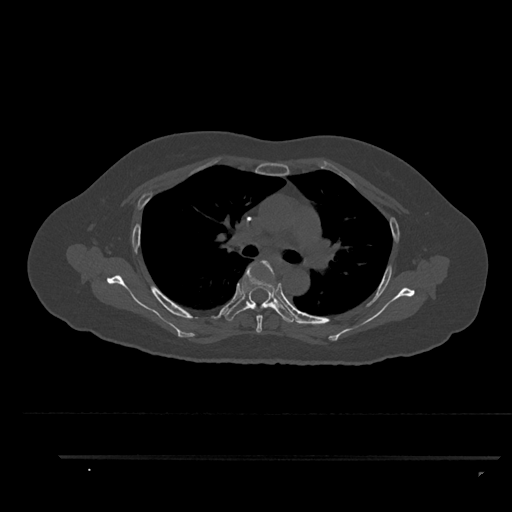
CT including the spine, one axial slice; slice 616 of 797 in the series (ordered by position); reconstruction kernel Br40s/3; 120 kVp; bone window (W 1800 / L 400 HU); 0.5 mm slice thickness; 512 × 512 image matrix. Female patient, age 44 years. From the clinical record (not read from this slice): primary cancer: renal; vertebrae with lytic lesions (as recorded): L1.
Outlined on this slice (semi-automatic segmentation, software-assisted and operator-edited):
- T4 vertebra: bounding box [x1, y1, x2, y2] px = [256, 260, 275, 333]
- T5 vertebra: [219, 261, 296, 323]